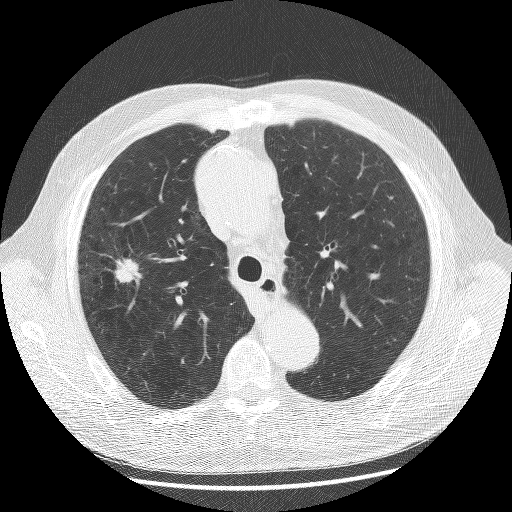
Chest CT (low-dose screening protocol), one axial image, baseline annual screen, lung window (W 1500 / L -600 HU), 2.5 mm slice thickness, 120 kVp, slice 46 of 175 in the series, 512 × 512 image matrix. Male participant, aged 70 years at enrolment.
- Expert reader's lesion annotation, bounding box [x1, y1, x2, y2] px = [75, 238, 149, 307].
- The screening reader recorded 2 non-calcified nodules or masses ≥4 mm on this exam (left upper lobe, right upper lobe); which of them this box marks is not recorded.
- Lung cancer was diagnosed 23 days after this screen: non-small cell carcinoma, right upper lobe, poorly differentiated (G3), stage IA (AJCC 6th edition), 20 mm at pathology.